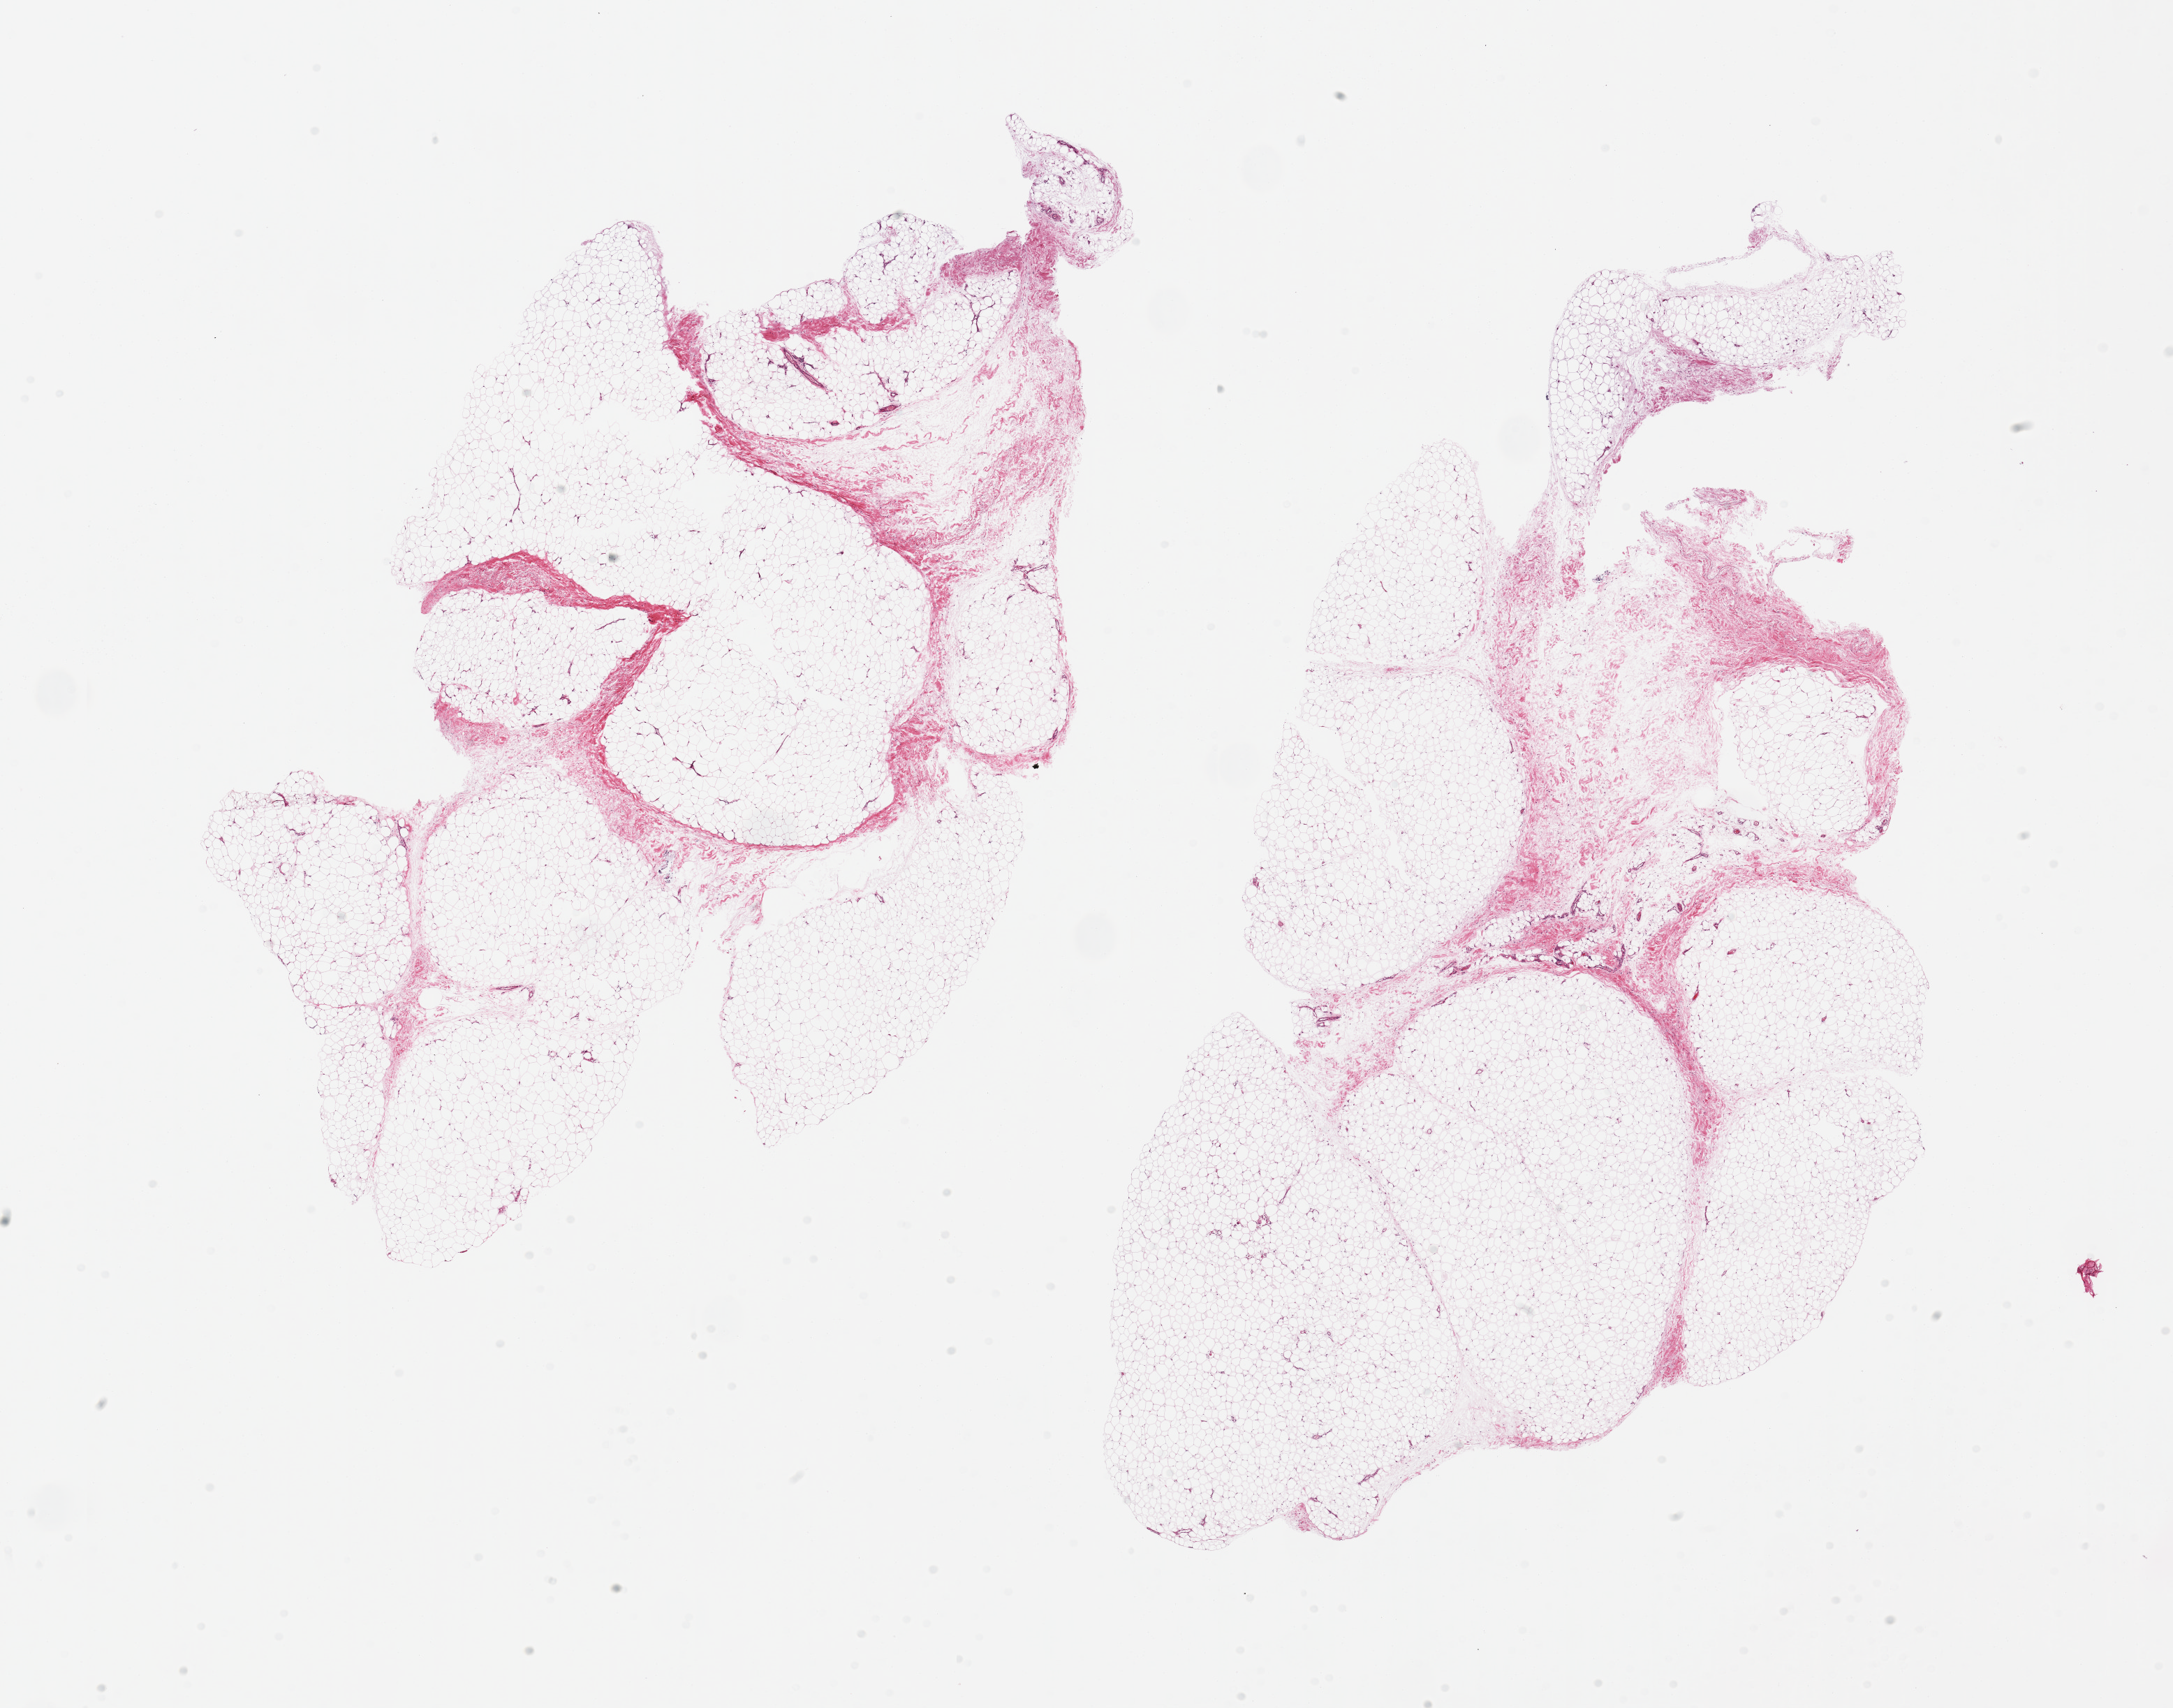
Whole-slide image, hematoxylin and eosin (H&E) stain — shown as a low-resolution overview of the whole scanned area (about 24.6 x 19.3 mm, from a 20x scan); PAXgene-fixed paraffin-embedded (PFPE) section; target tissue: adipose tissue; donor tissue sample. Donor sex: male.
* reviewer comment on this tissue sample: 2 pieces, fascia is ~20% tissue